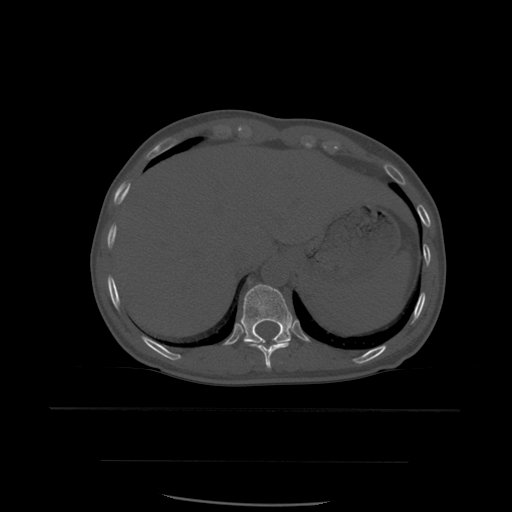
CT including the spine, one axial slice. Slice 303 of 574 in the series (ordered by position). Bone window (W 1800 / L 400 HU). 1.25 mm slice thickness. 512 × 512 image matrix. Patient age 48 years. Case-level facts recorded for this patient, not image findings: primary cancer: lung.
Outlined on this slice (semi-automatic segmentation, software-assisted and operator-edited):
- T10 vertebra: bounding box (x1, y1, x2, y2) in pixels: (247, 342, 291, 369)
- T11 vertebra: (241, 285, 293, 345)